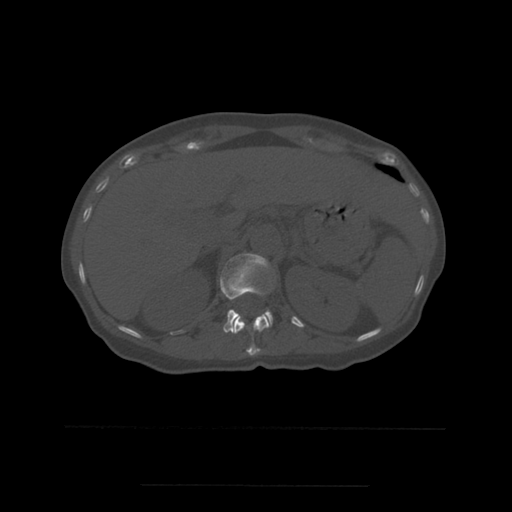
CT including the spine, one axial slice. Slice 247 of 544 in the series (ordered by position). Bone window (W 1800 / L 400 HU). 1.25 mm slice thickness. 512 × 512 image matrix, field of view 350 × 350 mm. Patient age 58 years. From the clinical record (not read from this slice): primary cancer: lung.
Annotated regions visible in this slice (semi-automatically segmented with operator editing):
- L1 vertebra: bounding box <220,253,274,333> (left, top, right, bottom; pixels)
- T12 vertebra: <233,315,271,356>